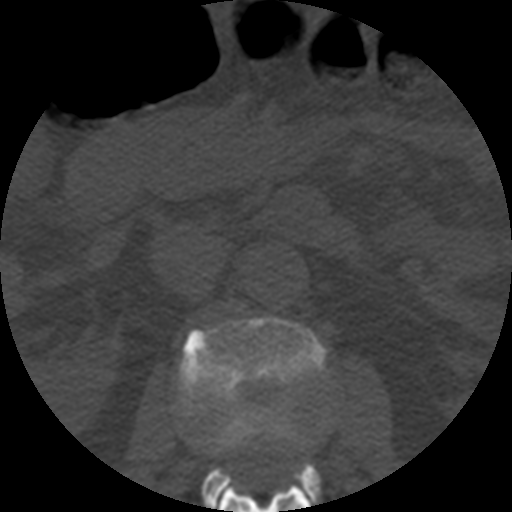
CT including the spine, one axial slice. Slice 168 of 508 in the series (ordered by position). Reconstruction kernel STANDARD. Bone window (W 1800 / L 400 HU). 512 × 512 image matrix, field of view 160 × 160 mm. Patient age 57 years. From the clinical record (not read from this slice): primary cancer: prostate.
Annotated regions visible in this slice (semi-automatic segmentation, software-assisted and operator-edited):
- L1 vertebra: bounding box <218,482,311,512> (left, top, right, bottom; pixels)
- L2 vertebra: <178,316,327,512>